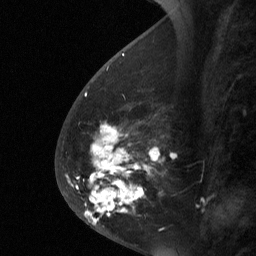
Breast MRI (dynamic contrast-enhanced), one sagittal slice; slice 23 of 64 in the series (ordered by position); dynamic contrast-enhanced study with each time point stored as its own series, time point 2 of 3 at this slice position (early post-contrast, ordered by acquisition time); 1.5 T; TE 4.8 ms, TR 27 ms; 2 mm slice thickness; 256 × 256 image matrix. Female patient, age 56 years. Case-level facts recorded for this patient, not image findings: setting: breast cancer imaged before/during neoadjuvant chemotherapy; receptor status: HER2-positive.
Annotated regions visible in this slice (semi-automatically segmented with operator editing):
- analysis volume of interest (the breast-tissue region the enhancement analysis was run in; not a lesion): bounding box <59,104,167,229> (left, top, right, bottom; pixels)
- tumour enhancement mask (voxels above the 90 % enhancement threshold inside the analysis volume of interest): <66,127,157,225>